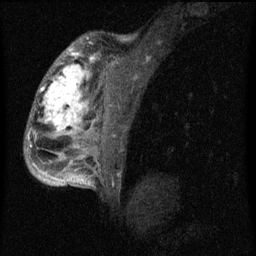
Breast MRI (dynamic contrast-enhanced), one sagittal slice. Slice 45 of 60 in the series (ordered by position). Dynamic contrast-enhanced series, image 2 of 4 at this slice position (ordered by acquisition). 1.5 T. TE 4.2 ms, TR 8 ms. 2 mm slice thickness. 256 × 256 image matrix, field of view 180 × 180 mm. Female patient, age 50 years.
Annotated regions visible in this slice (semi-automatic segmentation, software-assisted and operator-edited):
- analysis volume of interest (the breast-tissue region the enhancement analysis was run in; not a lesion): bounding box [x1, y1, x2, y2] px = [26, 44, 124, 177]
- tumour enhancement mask (voxels above the 70 % enhancement threshold inside the analysis volume of interest): [29, 46, 95, 177]